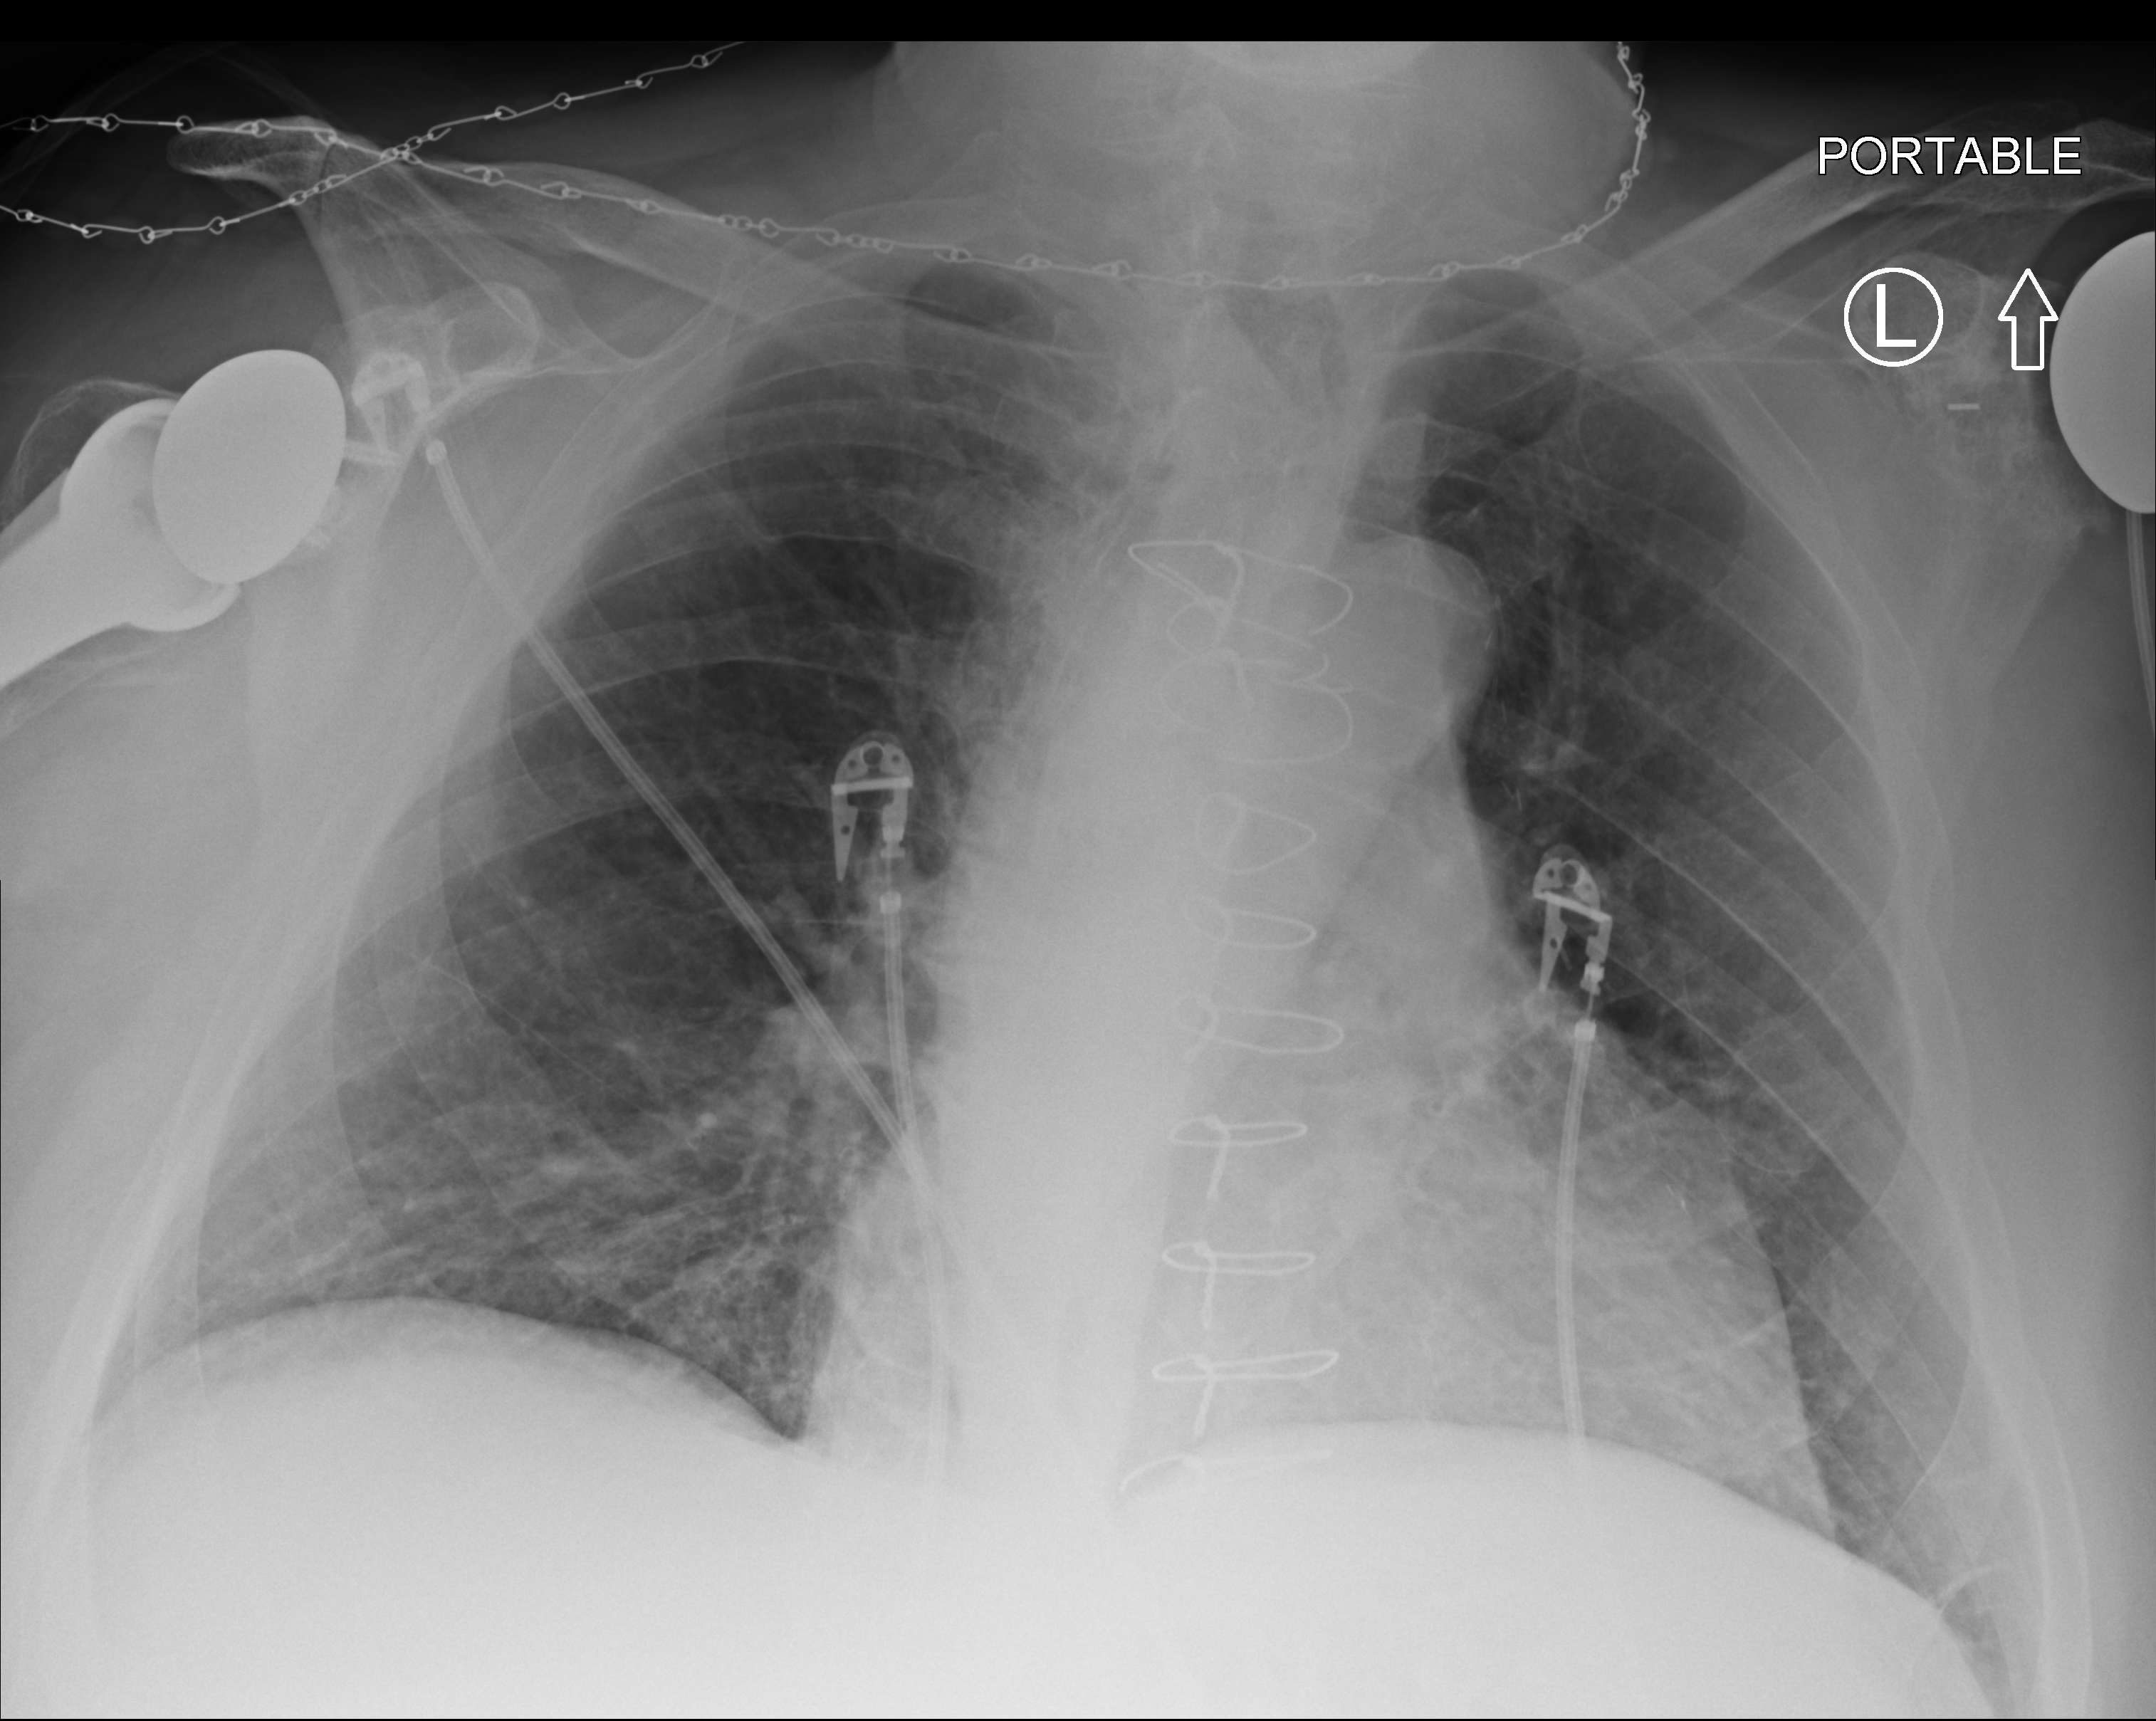
Chest X-ray (portable). Male patient hospitalised with COVID-19, age 60–74 years.
Hospital-stay facts (about this admission, not read from this image; timing relative to this image not recorded):
- mechanically ventilated during this hospital stay: no